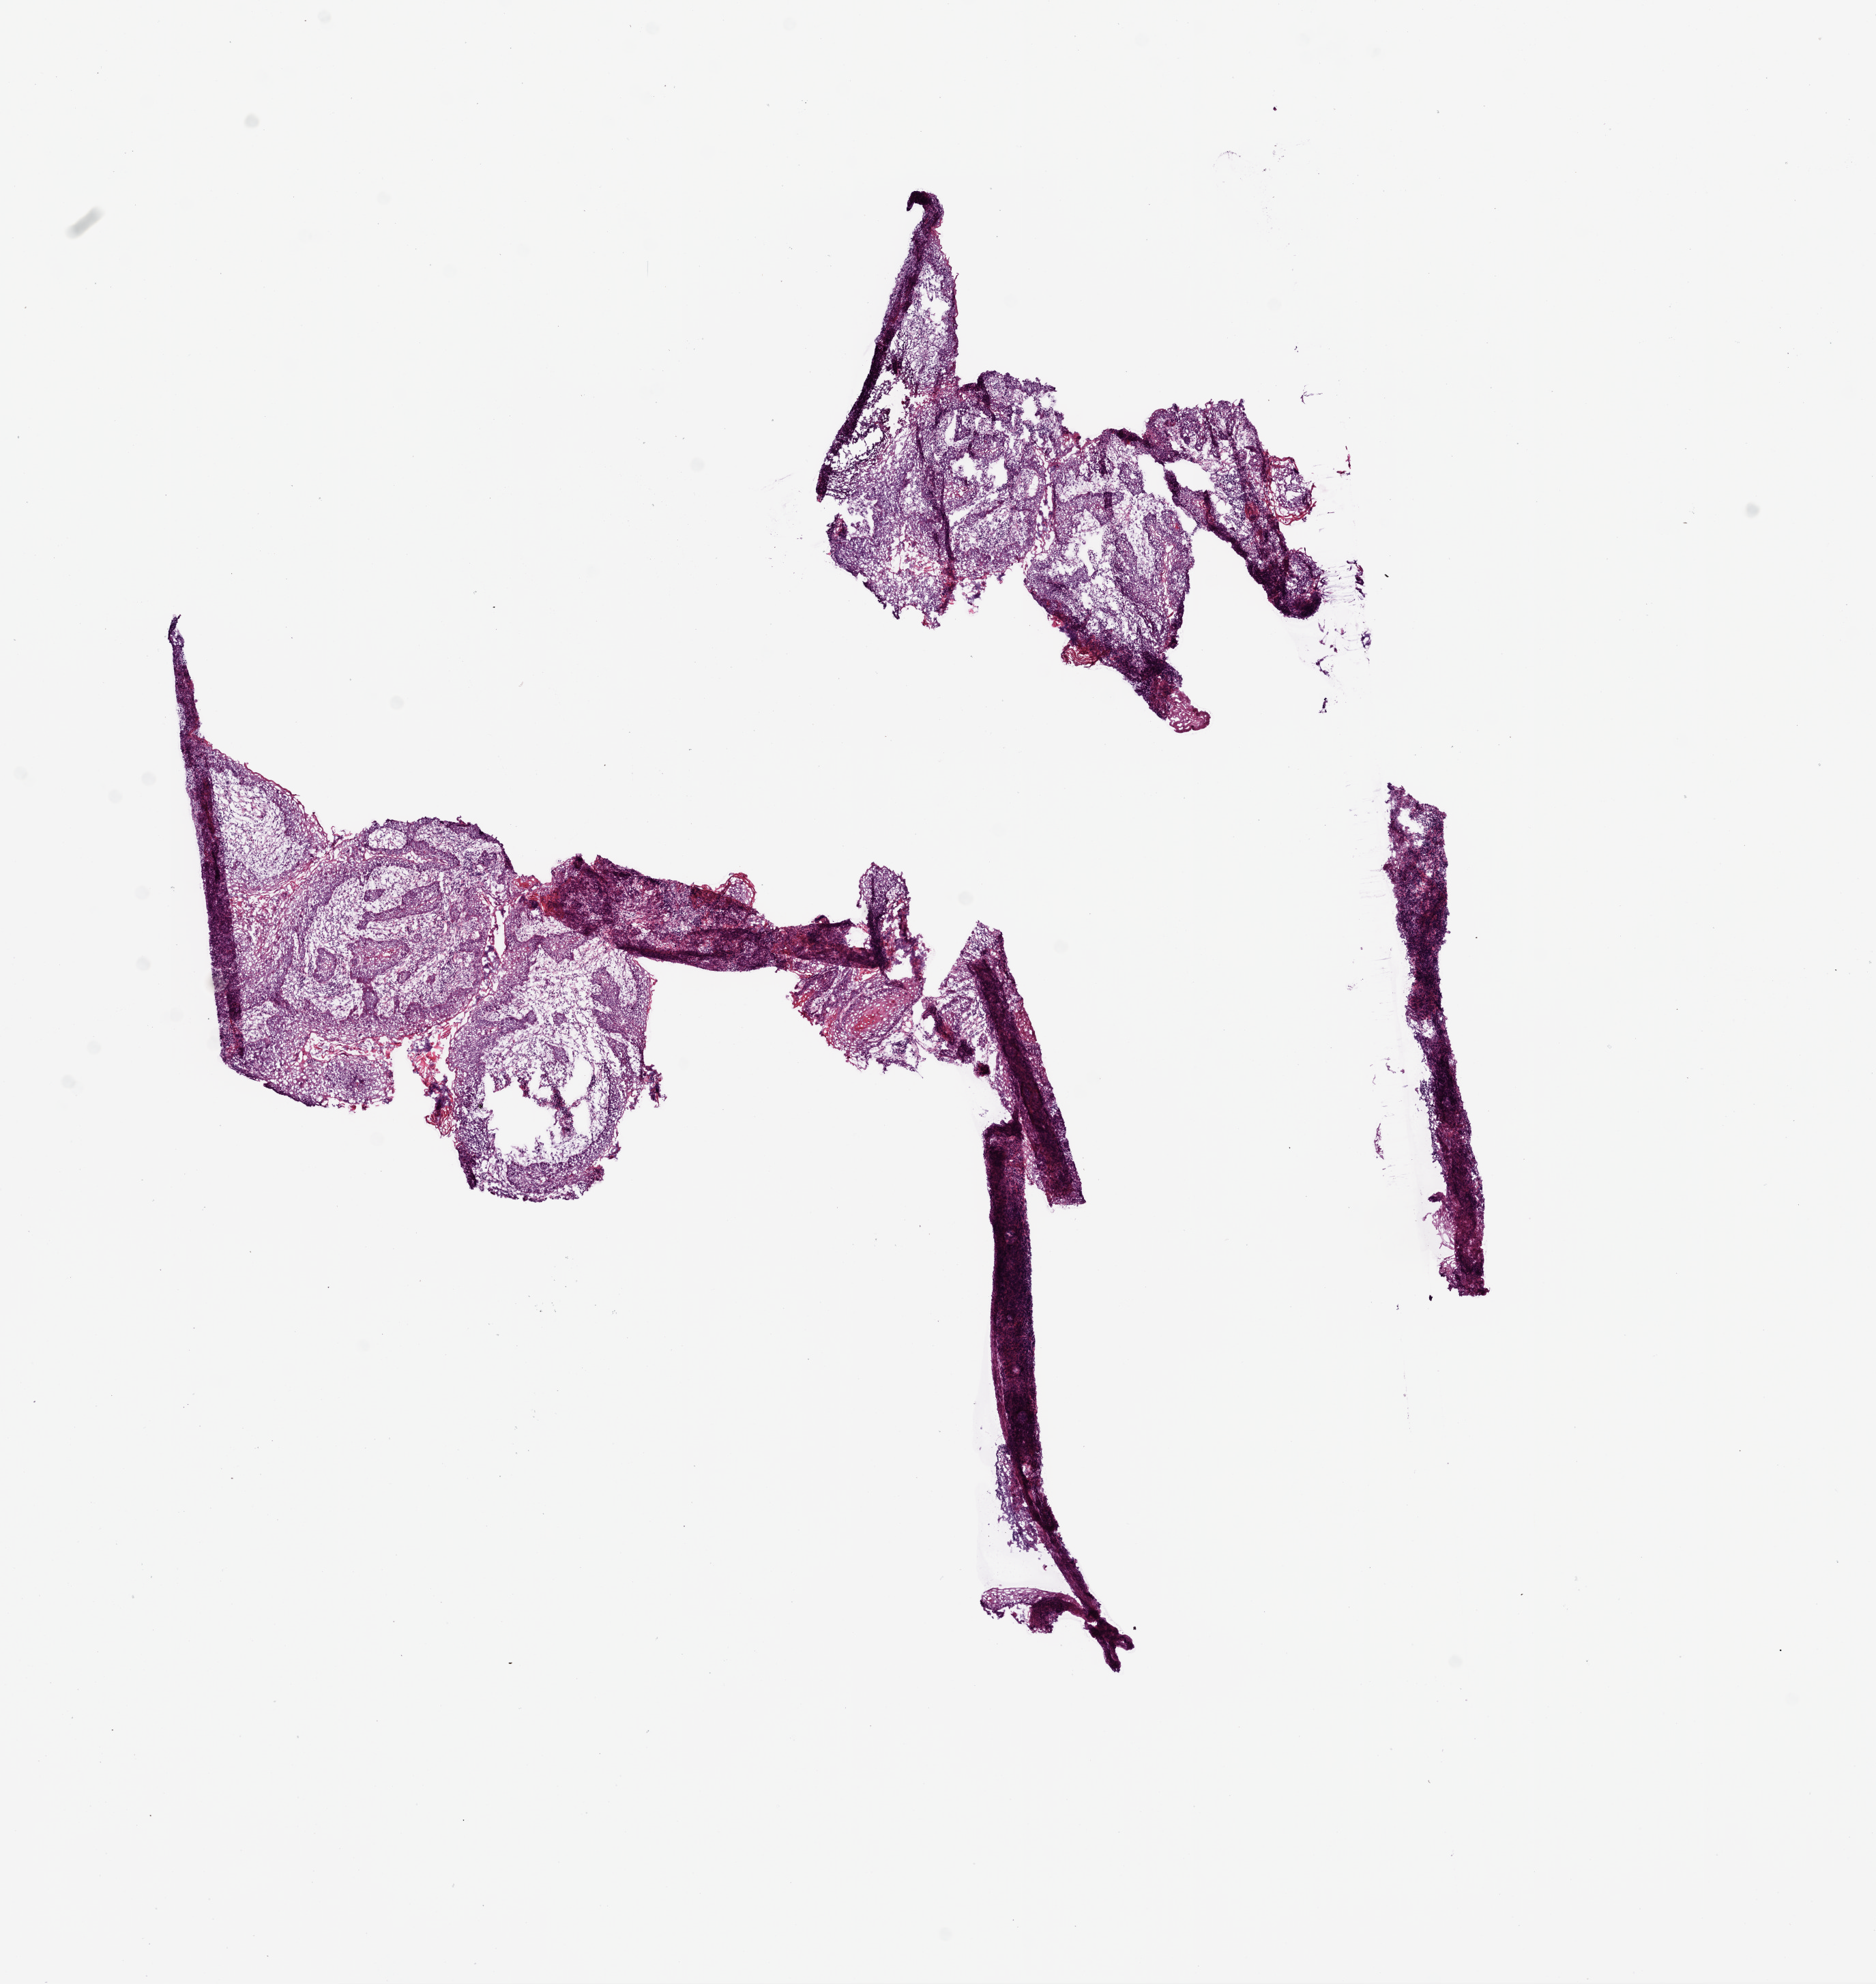
Whole-slide histology image, H&E-stained, low-resolution overview of the scanned area, about 11.0 x 11.7 mm, frozen section from the top of the tissue portion, sample: primary tumour, head and neck. Patient: male, age at initial diagnosis 73 years. Histologic grade: G2 (moderately differentiated). Composition of this section per pathologist review: tumour cells 85%, tumour nuclei 70%, normal cells 0%, stromal cells 15%, necrosis 0%.
AJCC pathologic stage: III (7th edition). Histologic diagnosis: Squamous cell carcinoma, NOS (overlapping lesion of lip, oral cavity and pharynx). Lymph nodes positive (case pathology): 1 of 24 examined.